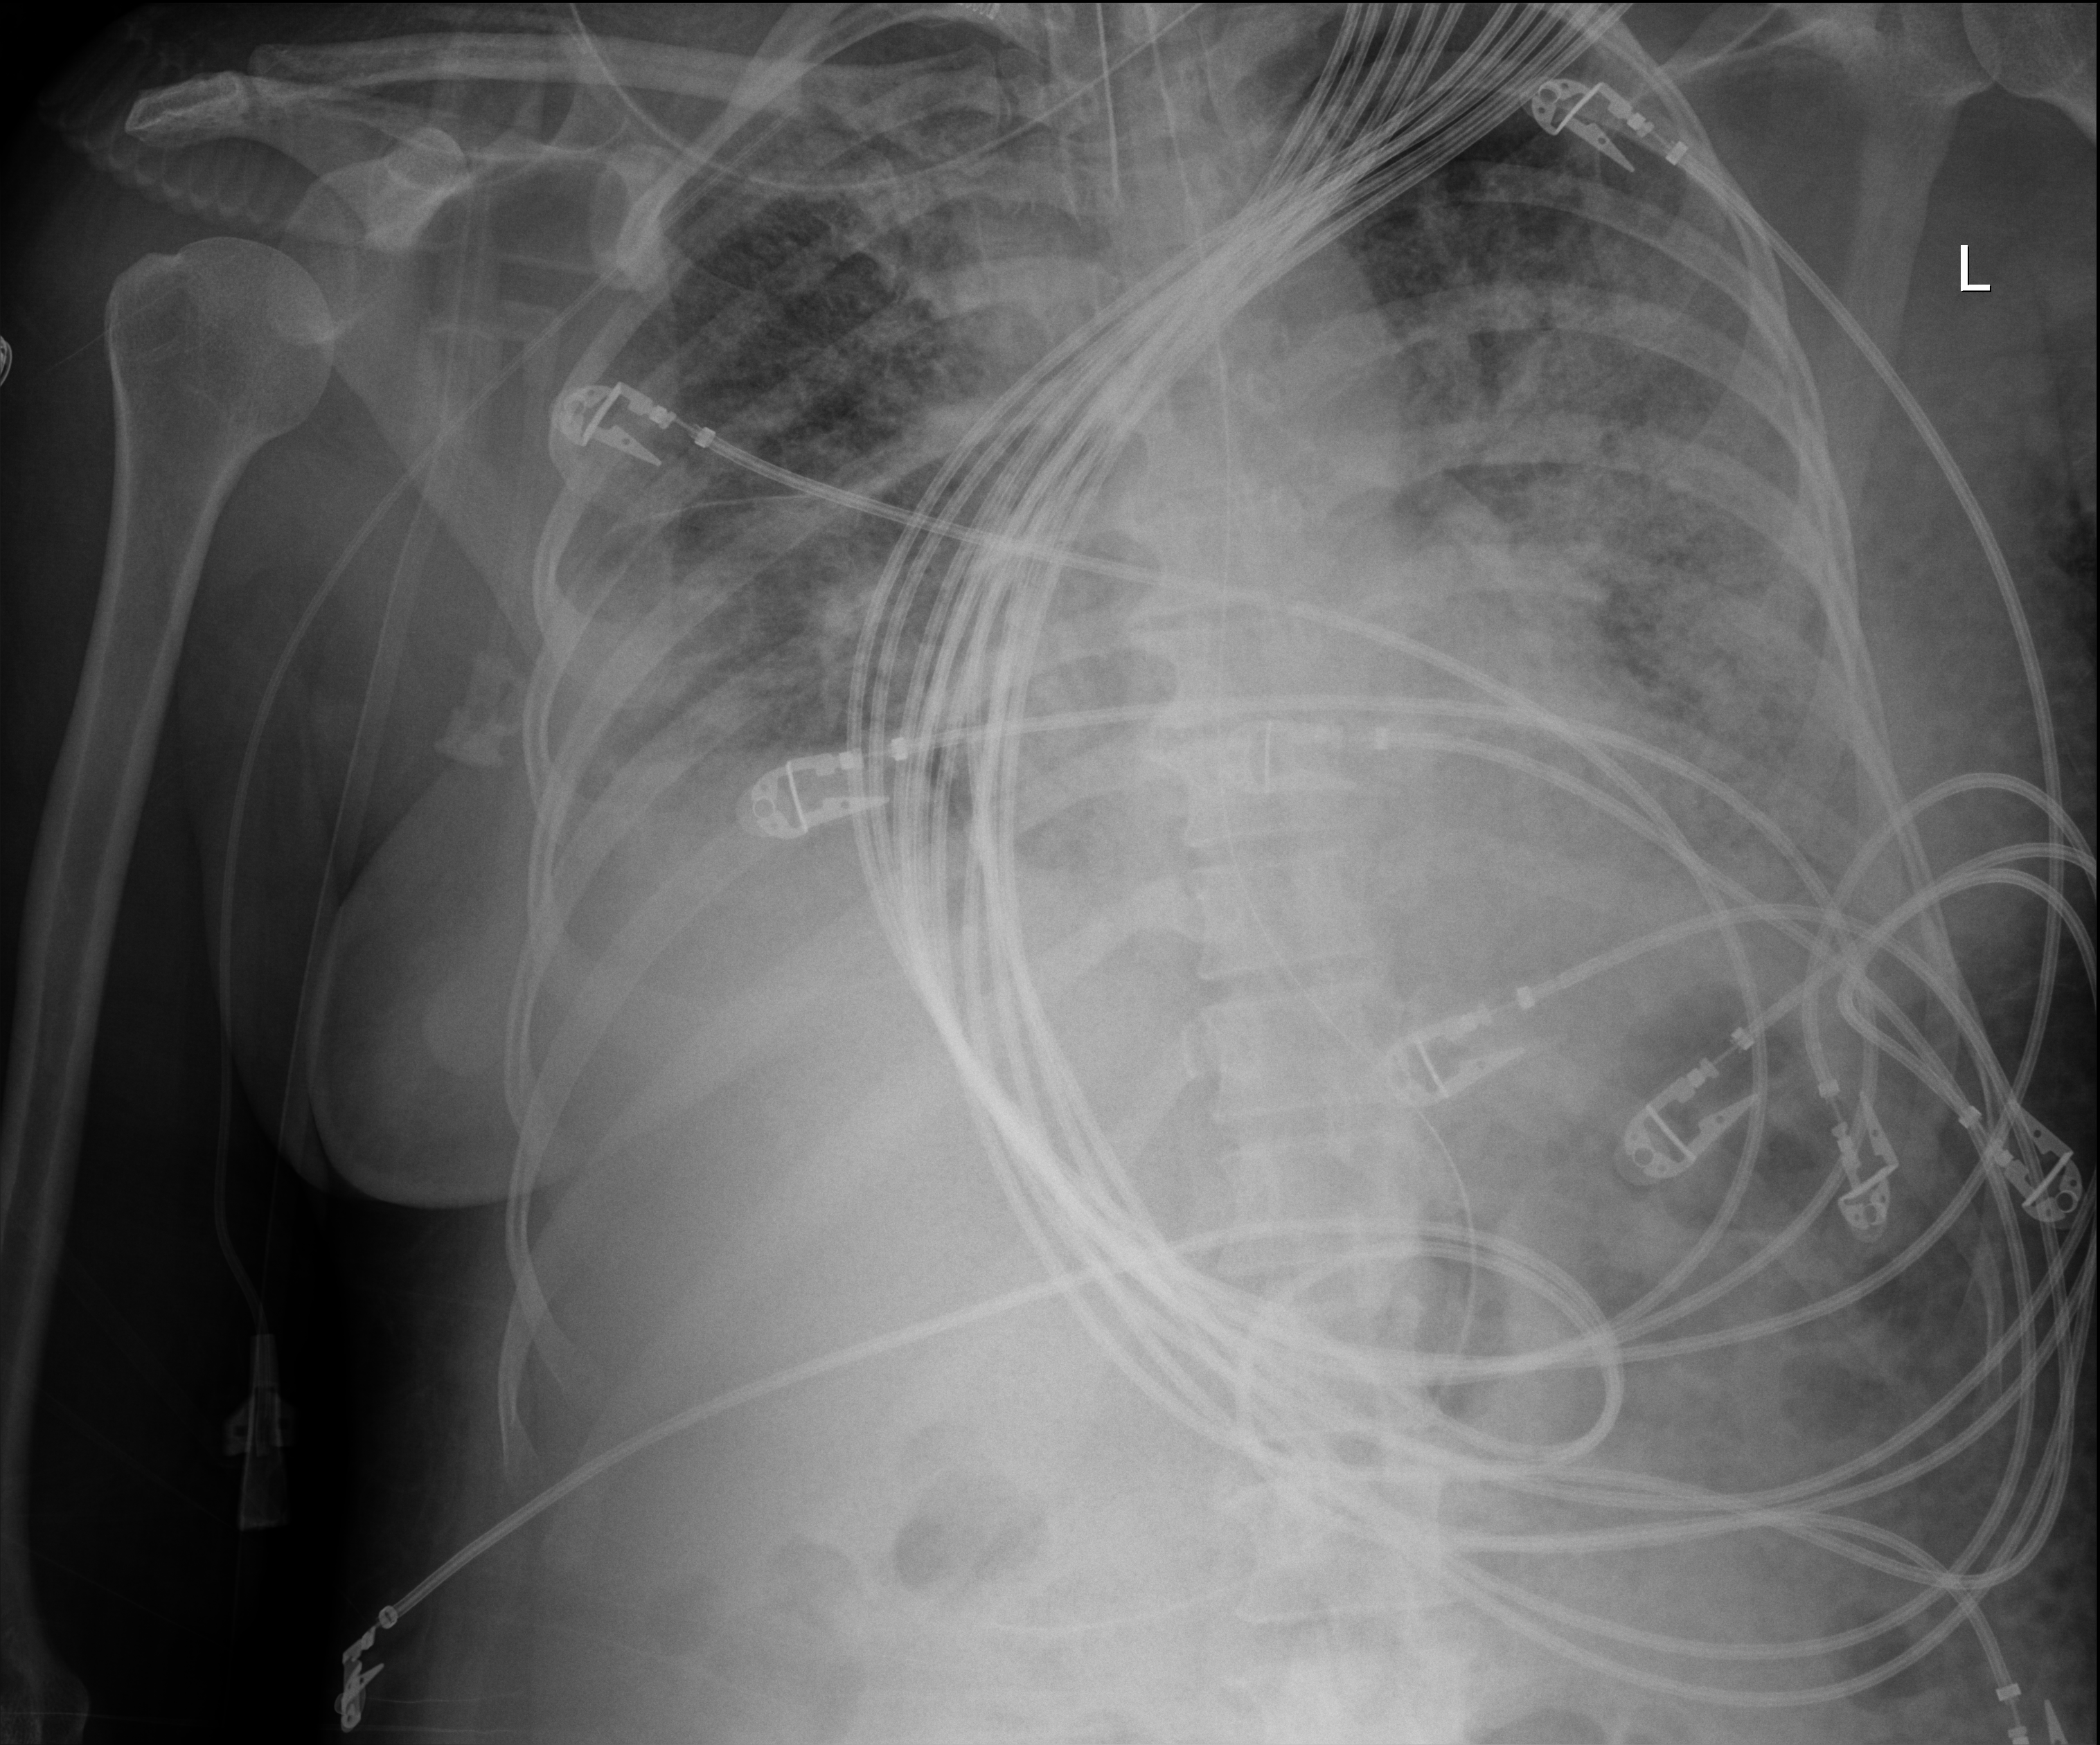
Chest radiograph (digital radiography), anteroposterior (AP) projection. Female patient hospitalised with COVID-19, age 18–59 years.
Admission-level facts for this patient (not findings on this image; timing relative to this image not recorded): mechanically ventilated during this hospital stay: yes; length of hospital stay: 71 days.